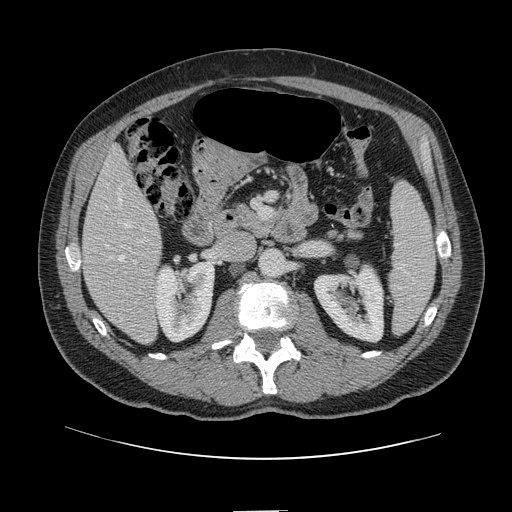
Contrast-enhanced abdominal CT, one axial slice; position 46 of 161 along the scan axis; intravenous contrast given; soft-tissue window (W 400 / L 40 HU); 2.5 mm slice thickness; 512 × 512 image matrix, field of view 412 × 412 mm. Male patient, age 66 years. From the clinical record (not read from this slice): diagnosis: colorectal cancer liver metastases, imaged before liver resection; multiple liver metastases: no.
Annotated regions visible in this slice (expert manual segmentation):
- hepatic veins: bounding box (x1, y1, x2, y2) in pixels: (119, 197, 128, 261)
- liver: (82, 151, 161, 344)
- planned liver remnant (the part of the liver to remain after resection): (82, 151, 157, 274)